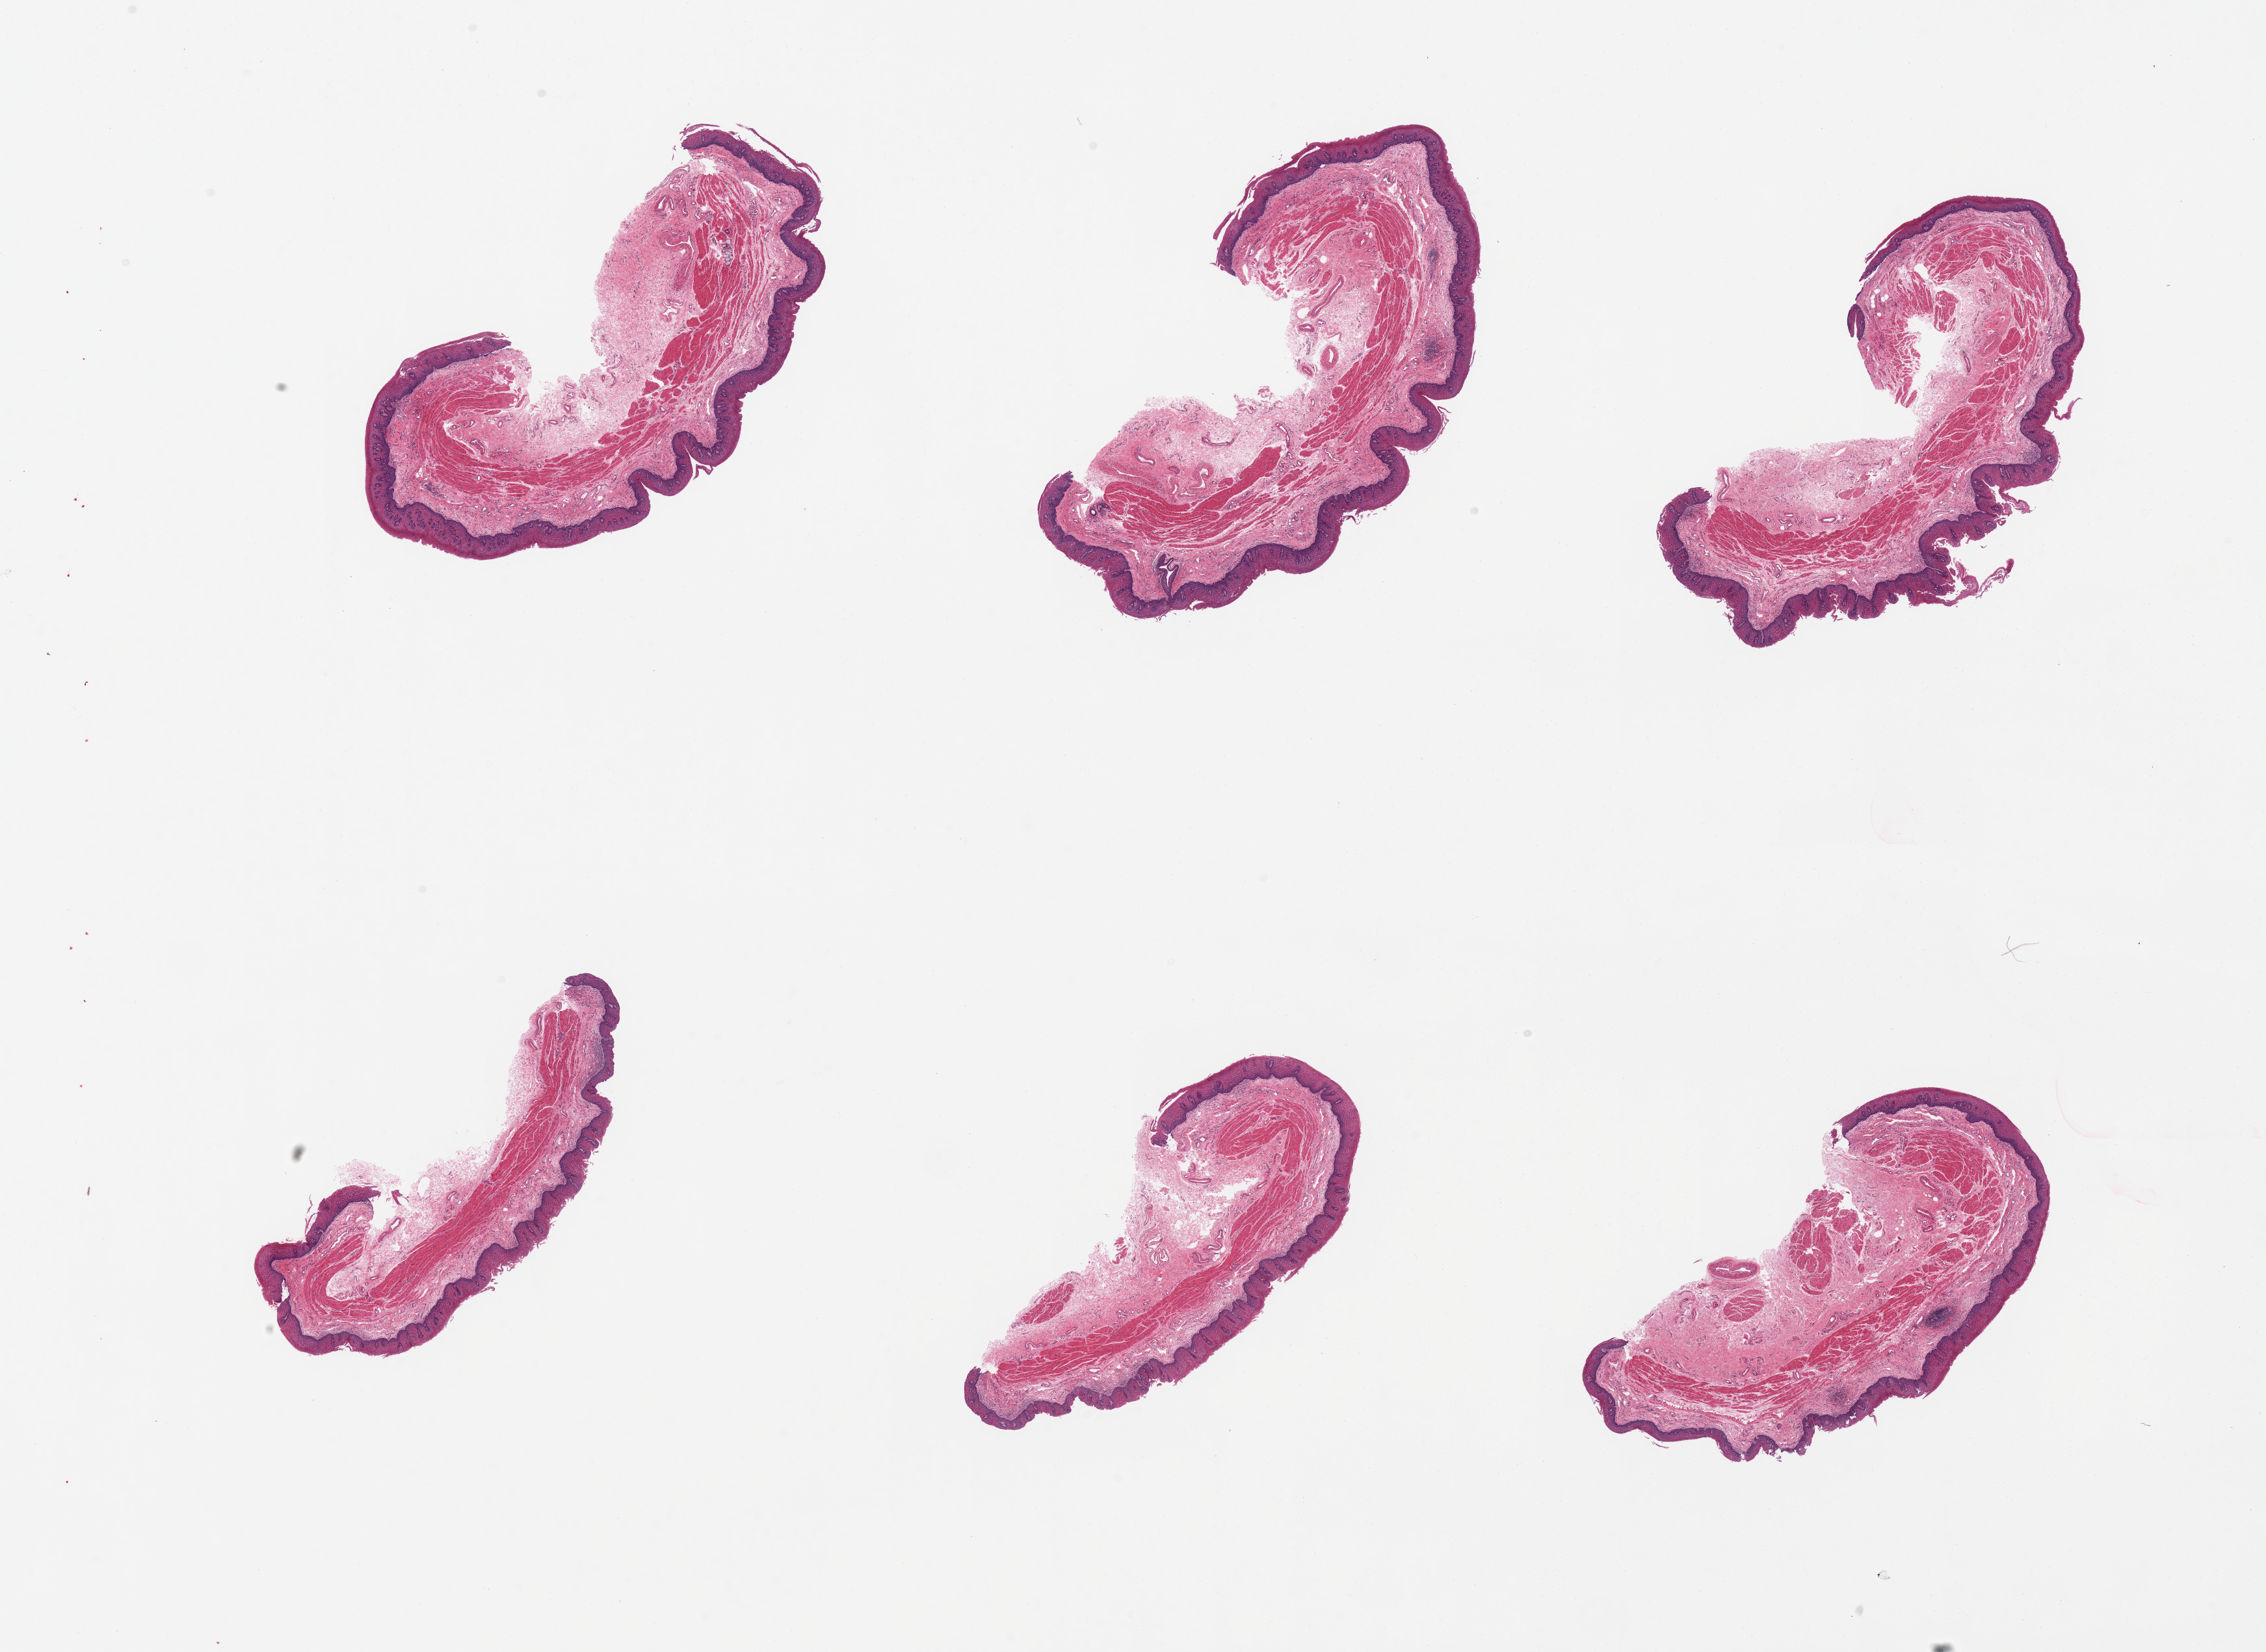
Whole-slide image, hematoxylin and eosin (H&E) stain, brightfield — a low-resolution overview of the entire scanned area, about 27.6 x 20.1 mm; PAXgene-fixed paraffin-embedded (PFPE) section; section of esophageal mucous membrane (target tissue); tissue donor sample. Donor sex: male.
* pathologist's review note for this sample: 6 pieces, all mucosa